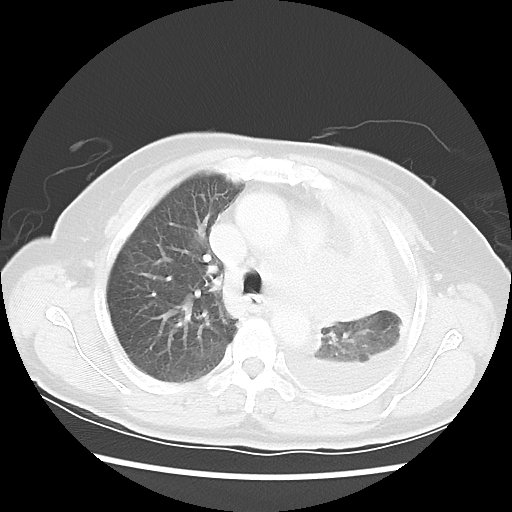
Chest CT, one axial slice. Slice 37 of 52 in the series (ordered by position). Reconstruction kernel LUNG. 120 kVp. Lung window (W 1500 / L -600 HU). 5 mm slice thickness. 512 × 512 image matrix, field of view 336 × 336 mm. Female patient, age 72 years. From the clinical record (not read from this slice): clinical TNM (as recorded): T4 N3 M1b; histopathological grade: G3.
Structures marked on this image (bounding box drawn by a radiologist):
- lung tumour (recorded histology: large cell carcinoma): bounding box <278,248,398,332> (left, top, right, bottom; pixels)